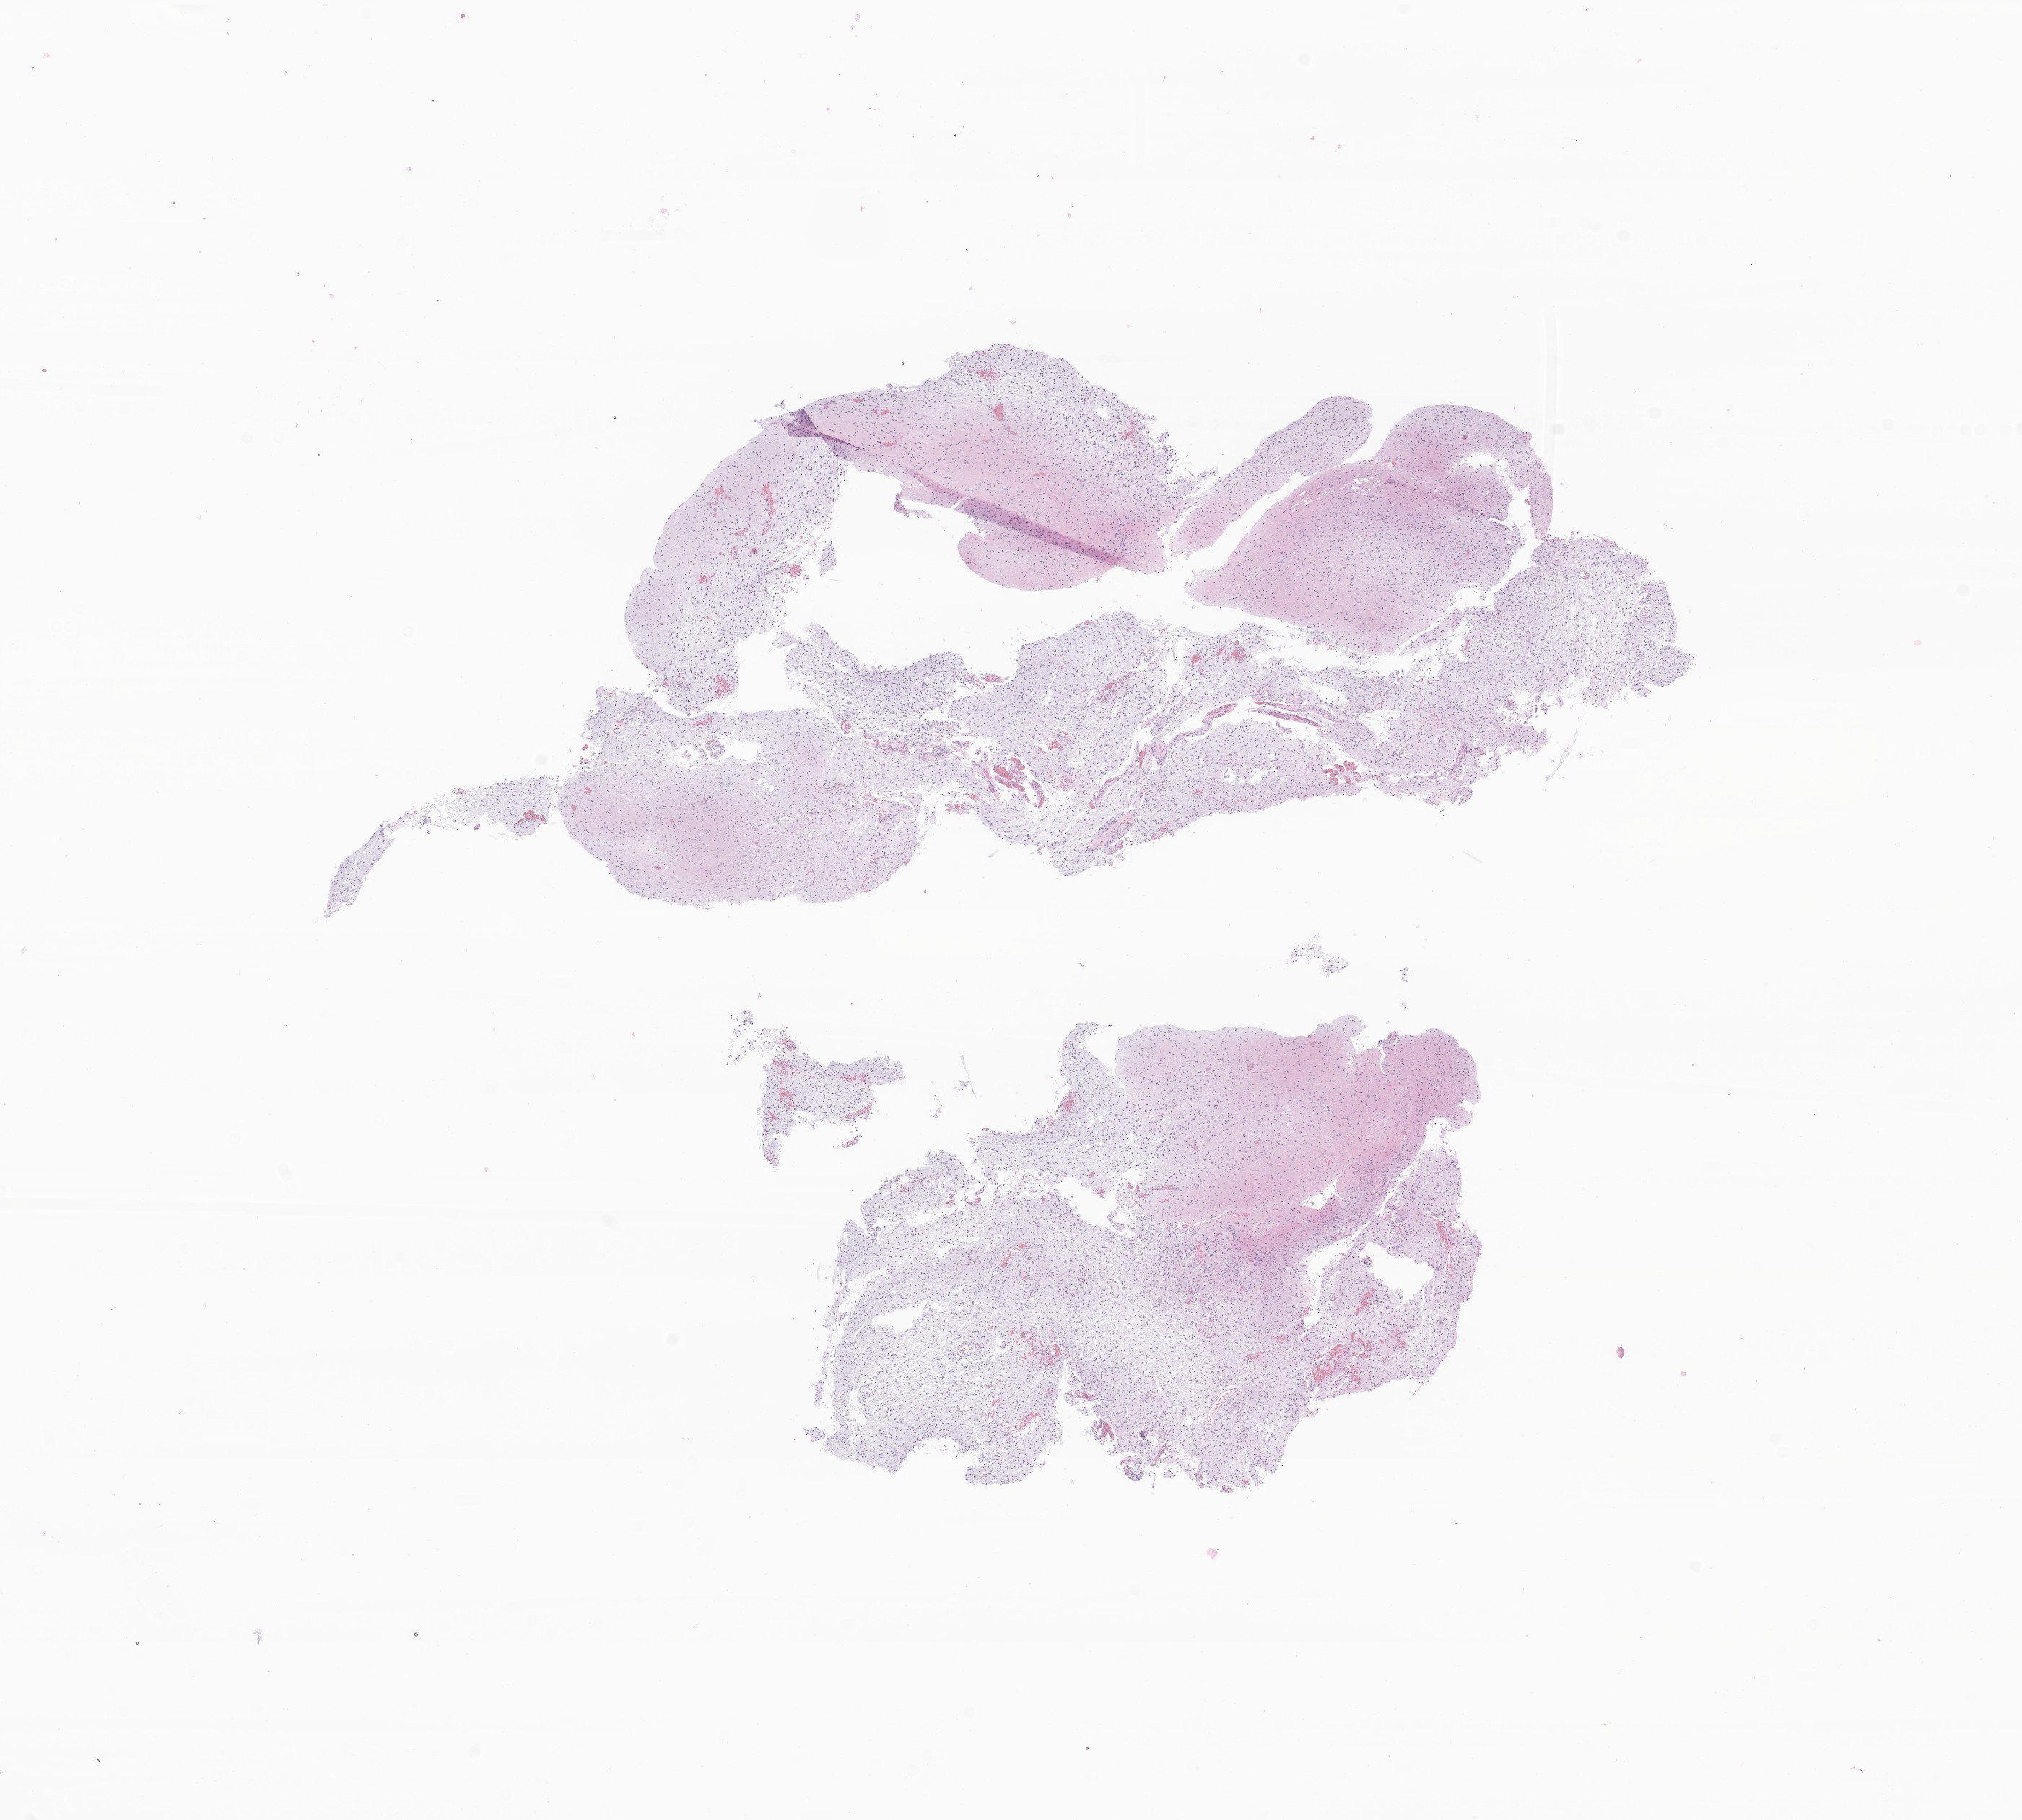
Hematoxylin and eosin (H&E) whole-slide image of tumor tissue from the spinal cord, a low-resolution overview of the entire scanned area, about 11.8 x 10.6 mm, FFPE section. Patient male; age 36 months (3 years).
• diagnosis (ICD-O-3 morphology term): Pilocytic astrocytoma